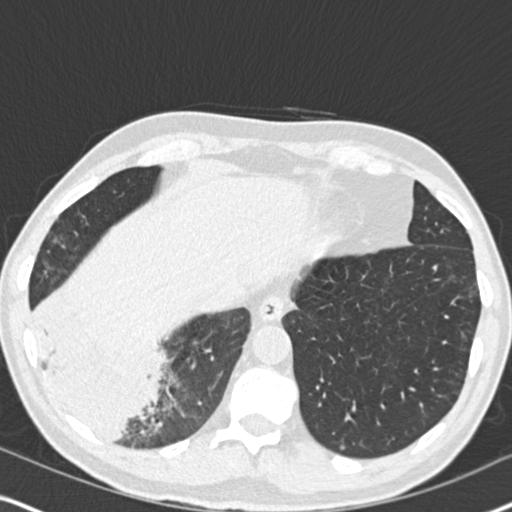
Axial slice from a low-dose chest CT screening exam. Second screening round (one year after baseline). Lung window (W 1500 / L -600 HU). Standard (soft-tissue) reconstruction kernel (B30f). Slice 129 of 182 in the series. Male participant, aged 61 years at enrolment. Current smoker at enrolment.
- Expert reader's lesion annotation, bounding box <22,284,181,456> (left, top, right, bottom; pixels).
- The exam's reader record, not a measurement of the box and not confirmed to be the same lesion: non-calcified nodule or mass ≥4 mm, right lower lobe, 90 × 80 mm, soft tissue attenuation, pre-existing on the prior screen: yes; interval growth: yes.
- Official screen result: positive, other.
- Participant outcome: lung cancer diagnosed 20 days after this screen — bronchiolo-alveolar adenocarcinoma, NOS, right lower lobe, moderately differentiated (G2), stage IIIB (AJCC 6th edition), 90 mm at pathology.